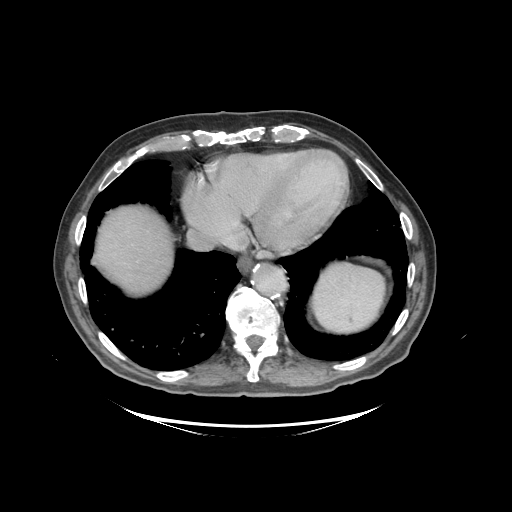
Contrast-enhanced abdominal CT (liver protocol), one axial slice. Slice 88 of 99 in the series (ordered by position). 140 kVp. Soft-tissue window (W 400 / L 40 HU). 2.5 mm slice thickness. 512 × 512 image matrix, field of view 460 × 460 mm. From the clinical record (not read from this slice): diagnosis: hepatocellular carcinoma (patient treated with transarterial chemoembolisation; whether this scan precedes or follows treatment is not stated here); TNM stage (as recorded): Stage-I; Child-Pugh class: A; tumour differentiation: moderately differentiated; tumour nodularity: uninodular.
Structures marked on this image (semi-automatically segmented with operator editing):
- abdominal aorta: bounding box <255,265,286,295> (left, top, right, bottom; pixels)
- liver parenchyma outside the tumour (the mass and vessels are separate outlines, so this box may not span the whole liver): <94,206,172,292>